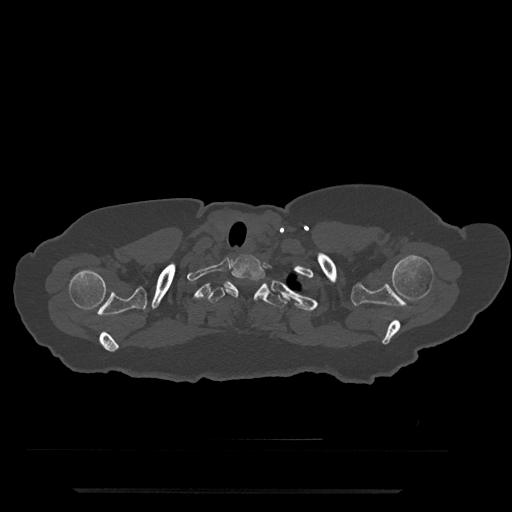
CT including the spine, one axial slice. Position 692 of 797 along the scan axis. 120 kVp. Bone window (W 1800 / L 400 HU). 0.5 mm slice thickness. 512 × 512 image matrix, field of view 440 × 440 mm. Patient: female, 51 years. From the clinical record (not read from this slice): primary cancer: neuro.
Outlined on this slice (semi-automatically segmented with operator editing):
- T1 vertebra: box from (x=223, y=254) to (x=265, y=298) px
- T2 vertebra: (x=207, y=281)–(x=286, y=309)